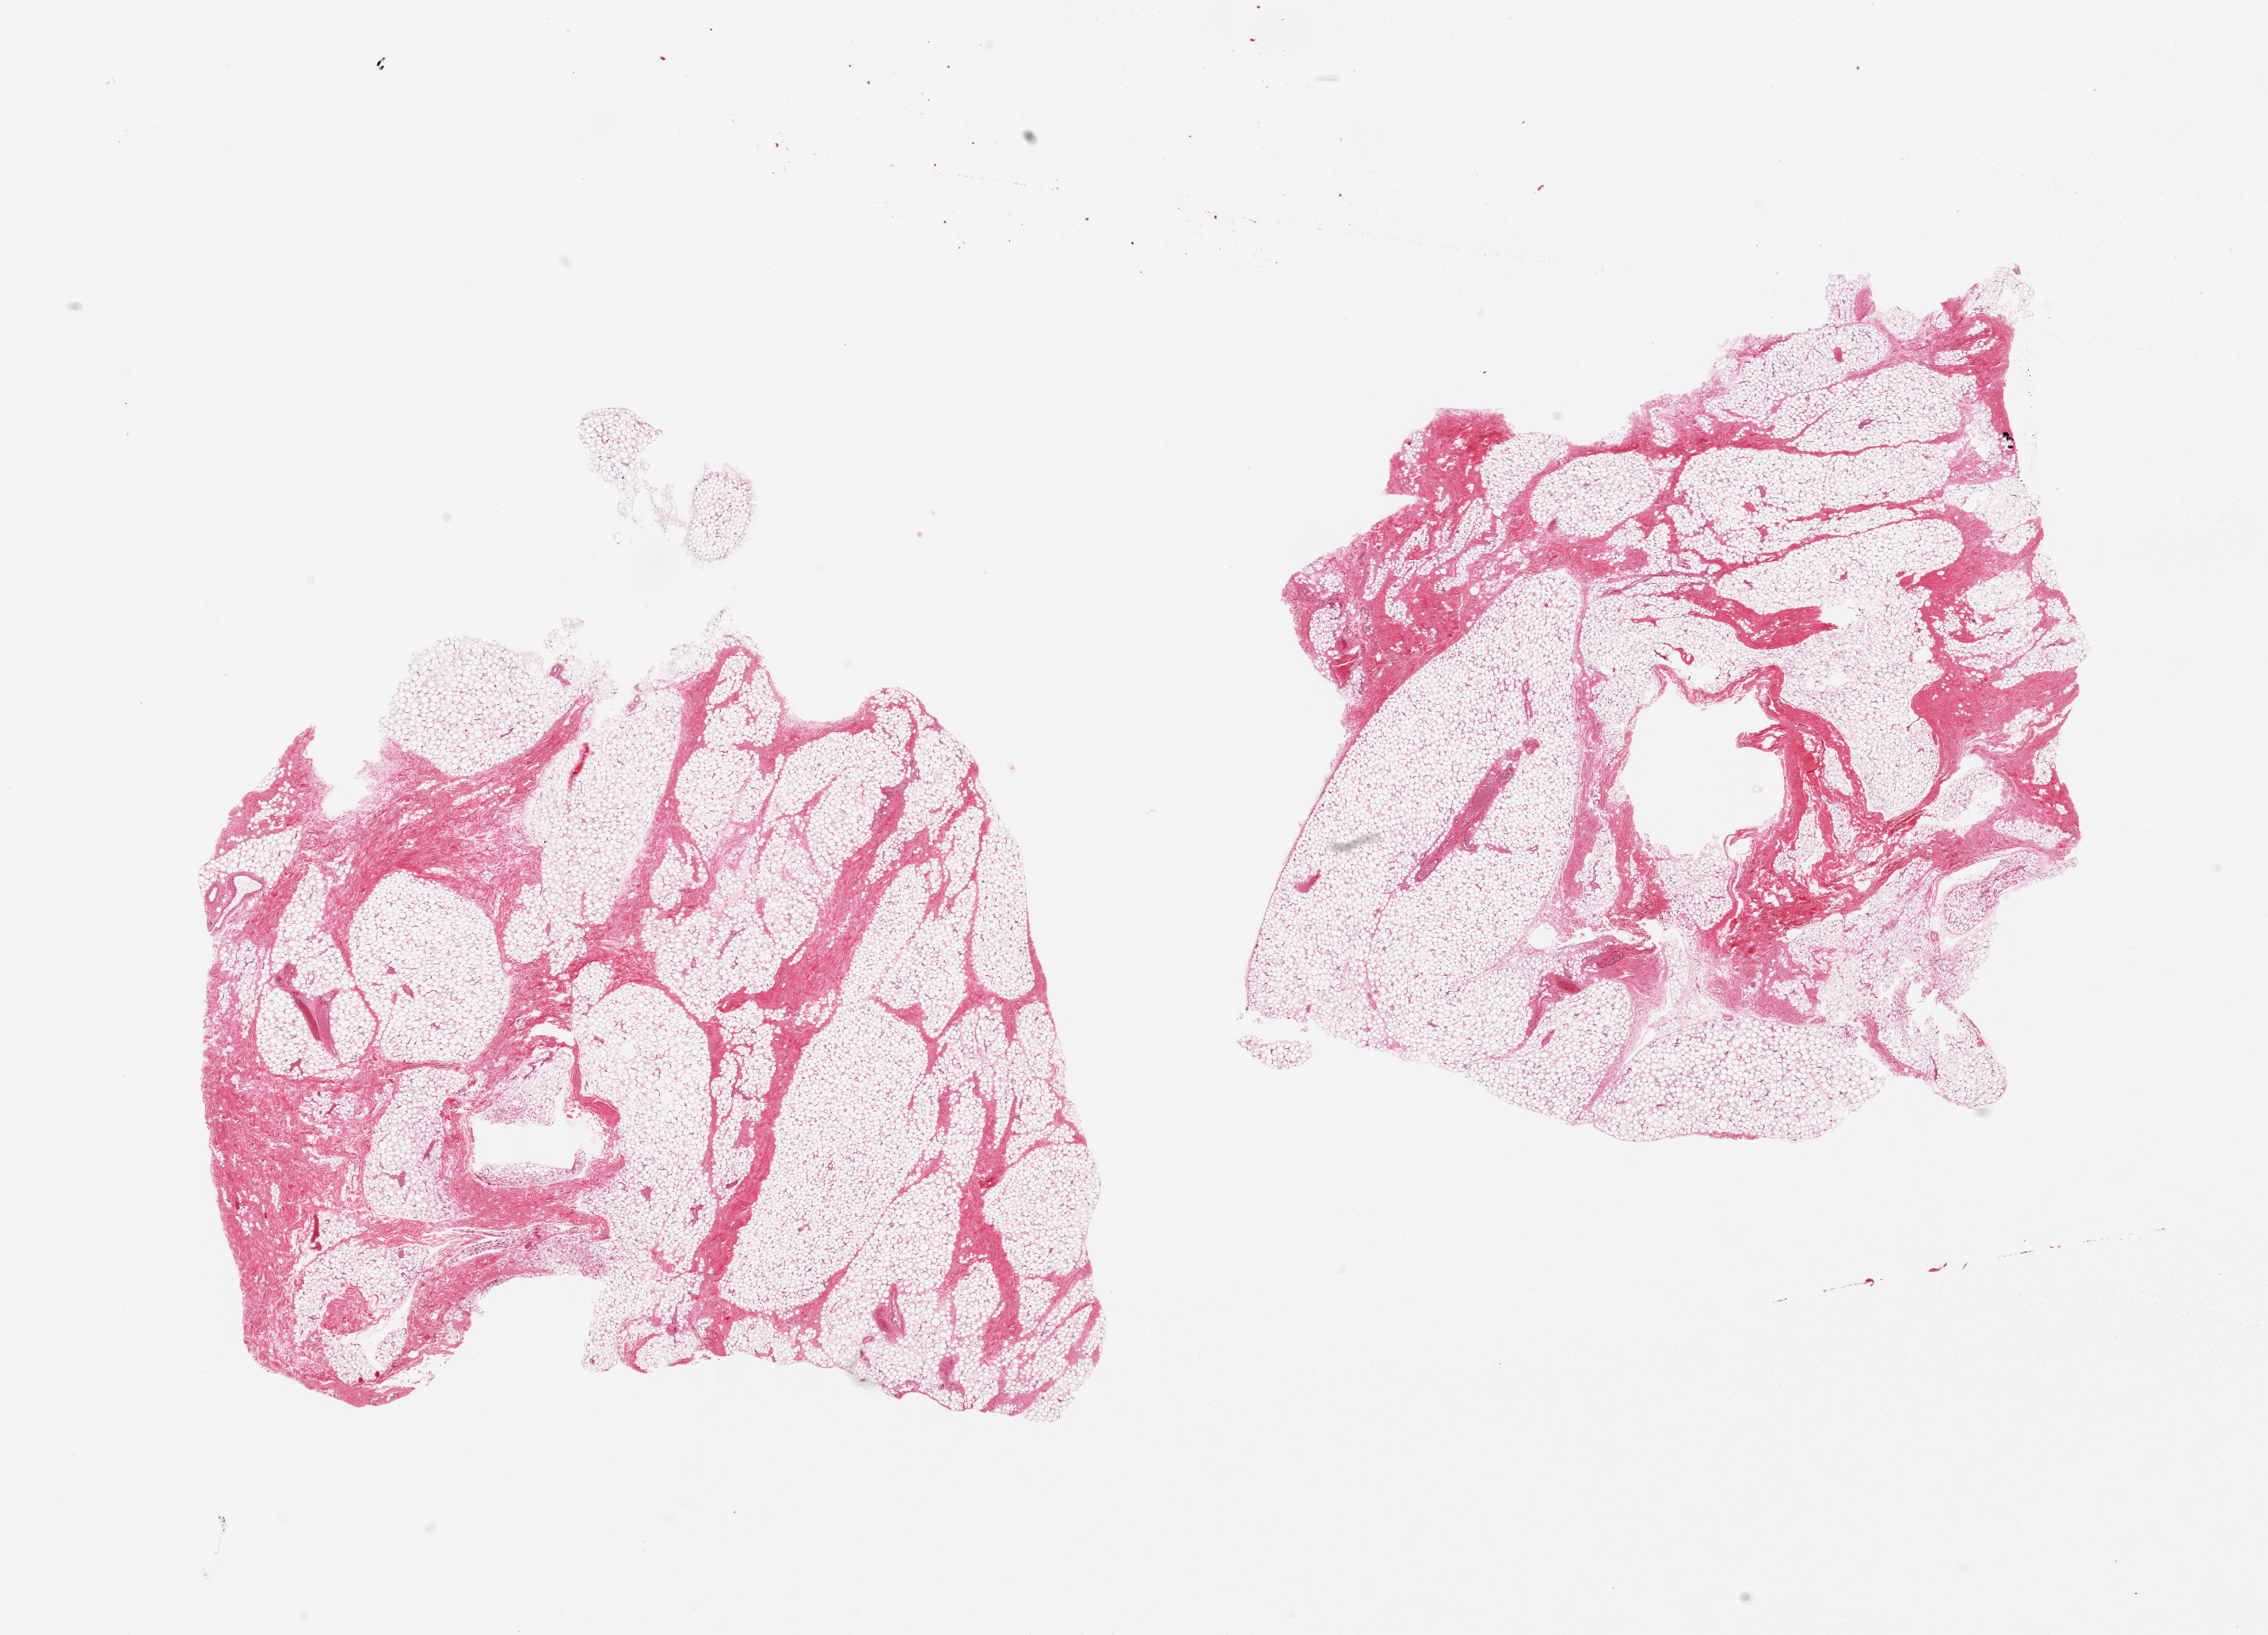
Digitized hematoxylin and eosin (H&E)-stained section — whole scanned area (about 22.6 x 16.3 mm, from a 20x scan) shown as a low-resolution overview; PAXgene-fixed paraffin-embedded (PFPE) section; section of breast (target tissue); donor tissue sample. Donor sex: male.
* reviewer comment on this tissue sample: 2 pieces; mature adipose tissue with fibrovascular component; no ductal structures observed